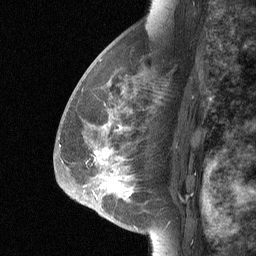
Breast MRI (dynamic contrast-enhanced), one sagittal slice; position 41 of 64 along the scan axis; dynamic contrast-enhanced study with each time point stored as its own series, time point 2 of 3 at this slice position (early post-contrast, ordered by acquisition time); 1.5 T; TE 4.8 ms, TR 27 ms; 256 × 256 image matrix, field of view 180 × 180 mm. Female patient, age 56 years. Case-level facts recorded for this patient, not image findings: setting: breast cancer imaged before/during neoadjuvant chemotherapy; receptor status: HER2-positive.
Outlined on this slice (semi-automatically segmented with operator editing):
- analysis volume of interest (the breast-tissue region the enhancement analysis was run in; not a lesion): bounding box <68,83,167,214> (left, top, right, bottom; pixels)
- tumour enhancement mask (voxels above the 90 % enhancement threshold inside the analysis volume of interest): <102,148,129,195>